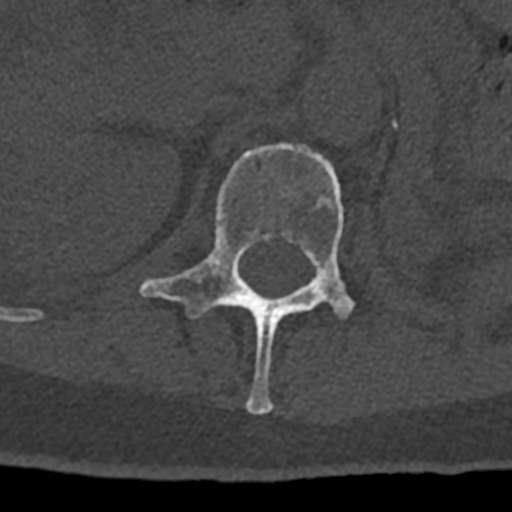
CT including the spine, one axial slice; 120 kVp; bone window (W 1800 / L 400 HU); 0.5 mm slice thickness; 512 × 512 image matrix, field of view 160 × 160 mm. Patient: male, 74 years. From the clinical record (not read from this slice): primary cancer: renal; vertebrae with lytic lesions (as recorded): T10, L1, L2, L3, L4, L5.
Annotated regions visible in this slice (semi-automatically segmented with operator editing):
- L1 vertebra: box from (x=140, y=143) to (x=355, y=414) px